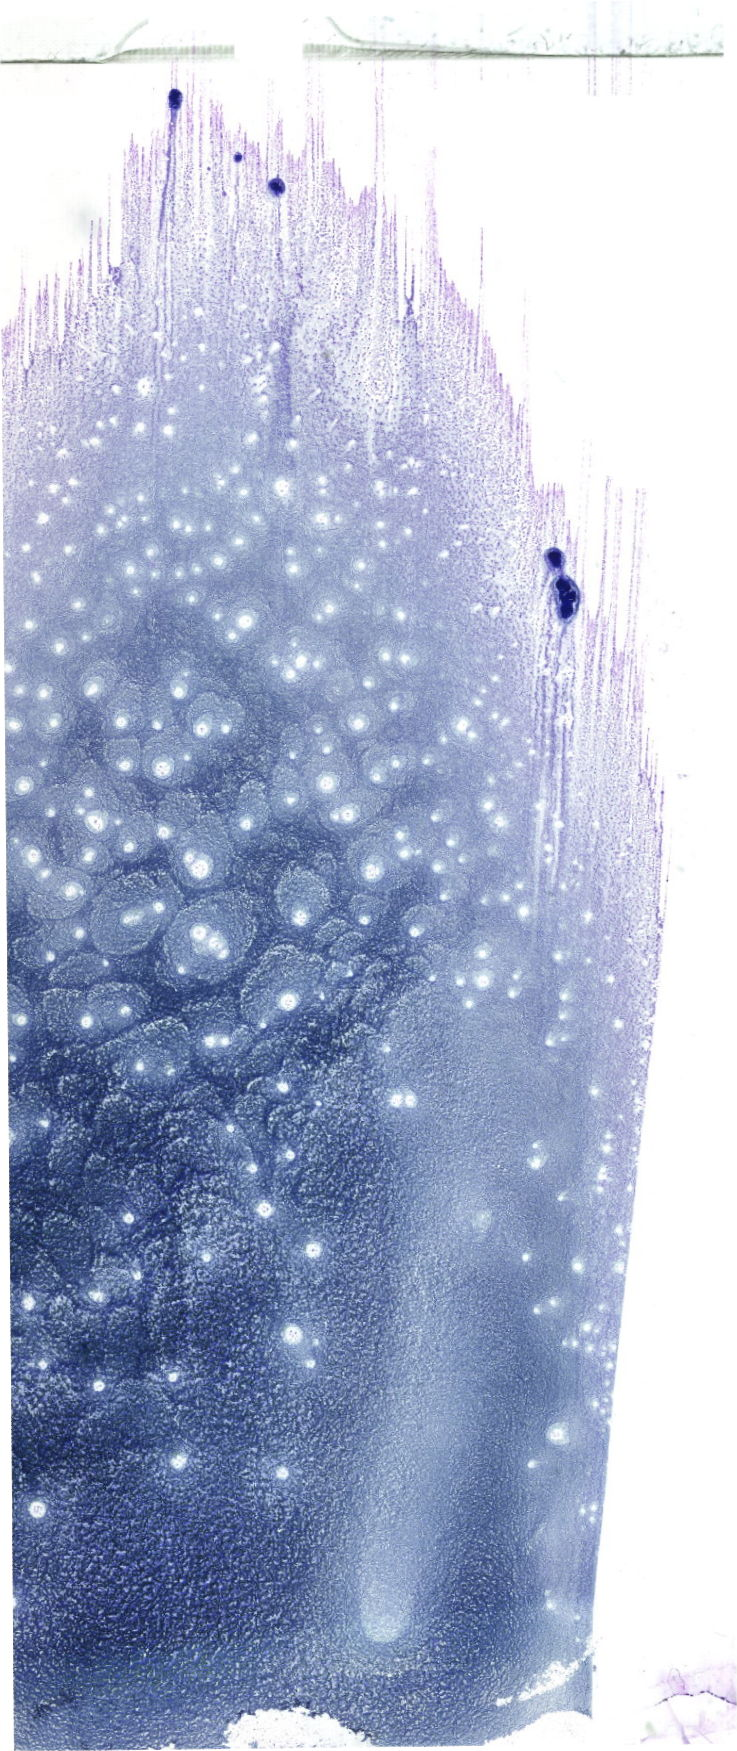
Whole-slide image of a May-Grünwald–Giemsa-stained bone marrow aspirate smear, a low-resolution overview of the entire scanned area, about 20.9 x 49.6 mm. Patient sex: female.
Diagnosis: B Acute Lymphoblastic Leukemia.